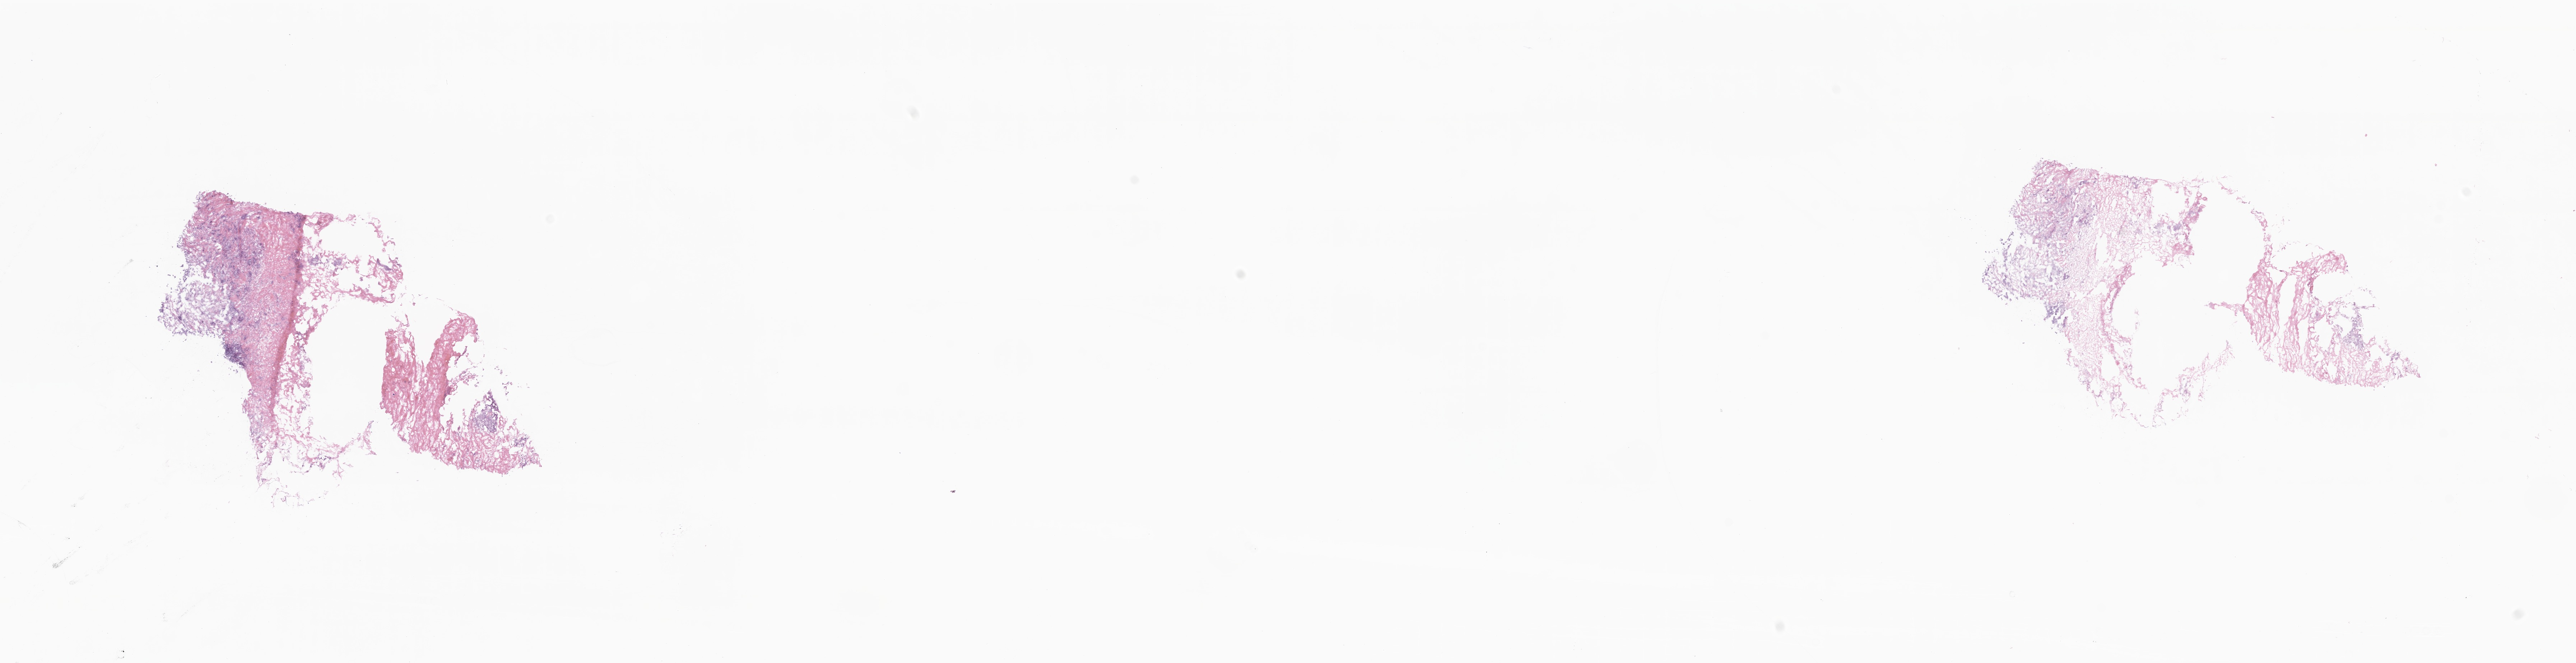
Haematoxylin and eosin whole-slide image, shown as a low-resolution overview of the whole scanned area (about 30.2 x 7.8 mm); frozen section (tissue freezing medium); primary tumor; anatomic site: breast (left). Female, age 51 years at initial diagnosis. Slide review estimates, as recorded: tumor cells 25%, tumor nuclei 90%, stromal cells 74%, necrosis 1%, normal cells 0%. Inflammatory infiltration, as recorded: lymphocyte infiltration 5%, monocyte infiltration 0%, neutrophil infiltration 0%.
Diagnosis: Infiltrating duct carcinoma, NOS.